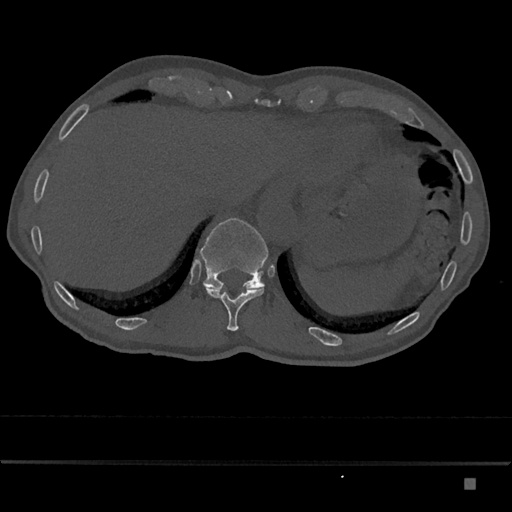
CT including the spine, one axial slice; slice 649 of 797 in the series (ordered by position); reconstruction kernel Br40s/3; 120 kVp; bone window (W 1800 / L 400 HU); 0.5 mm slice thickness; 512 × 512 image matrix, field of view 390 × 390 mm. Patient: male, 72 years. Case-level facts recorded for this patient, not image findings: primary cancer: prostate.
Annotated regions visible in this slice (semi-automatic segmentation, software-assisted and operator-edited):
- T11 vertebra: bounding box [x1, y1, x2, y2] px = [204, 285, 265, 331]
- T12 vertebra: [199, 218, 268, 289]